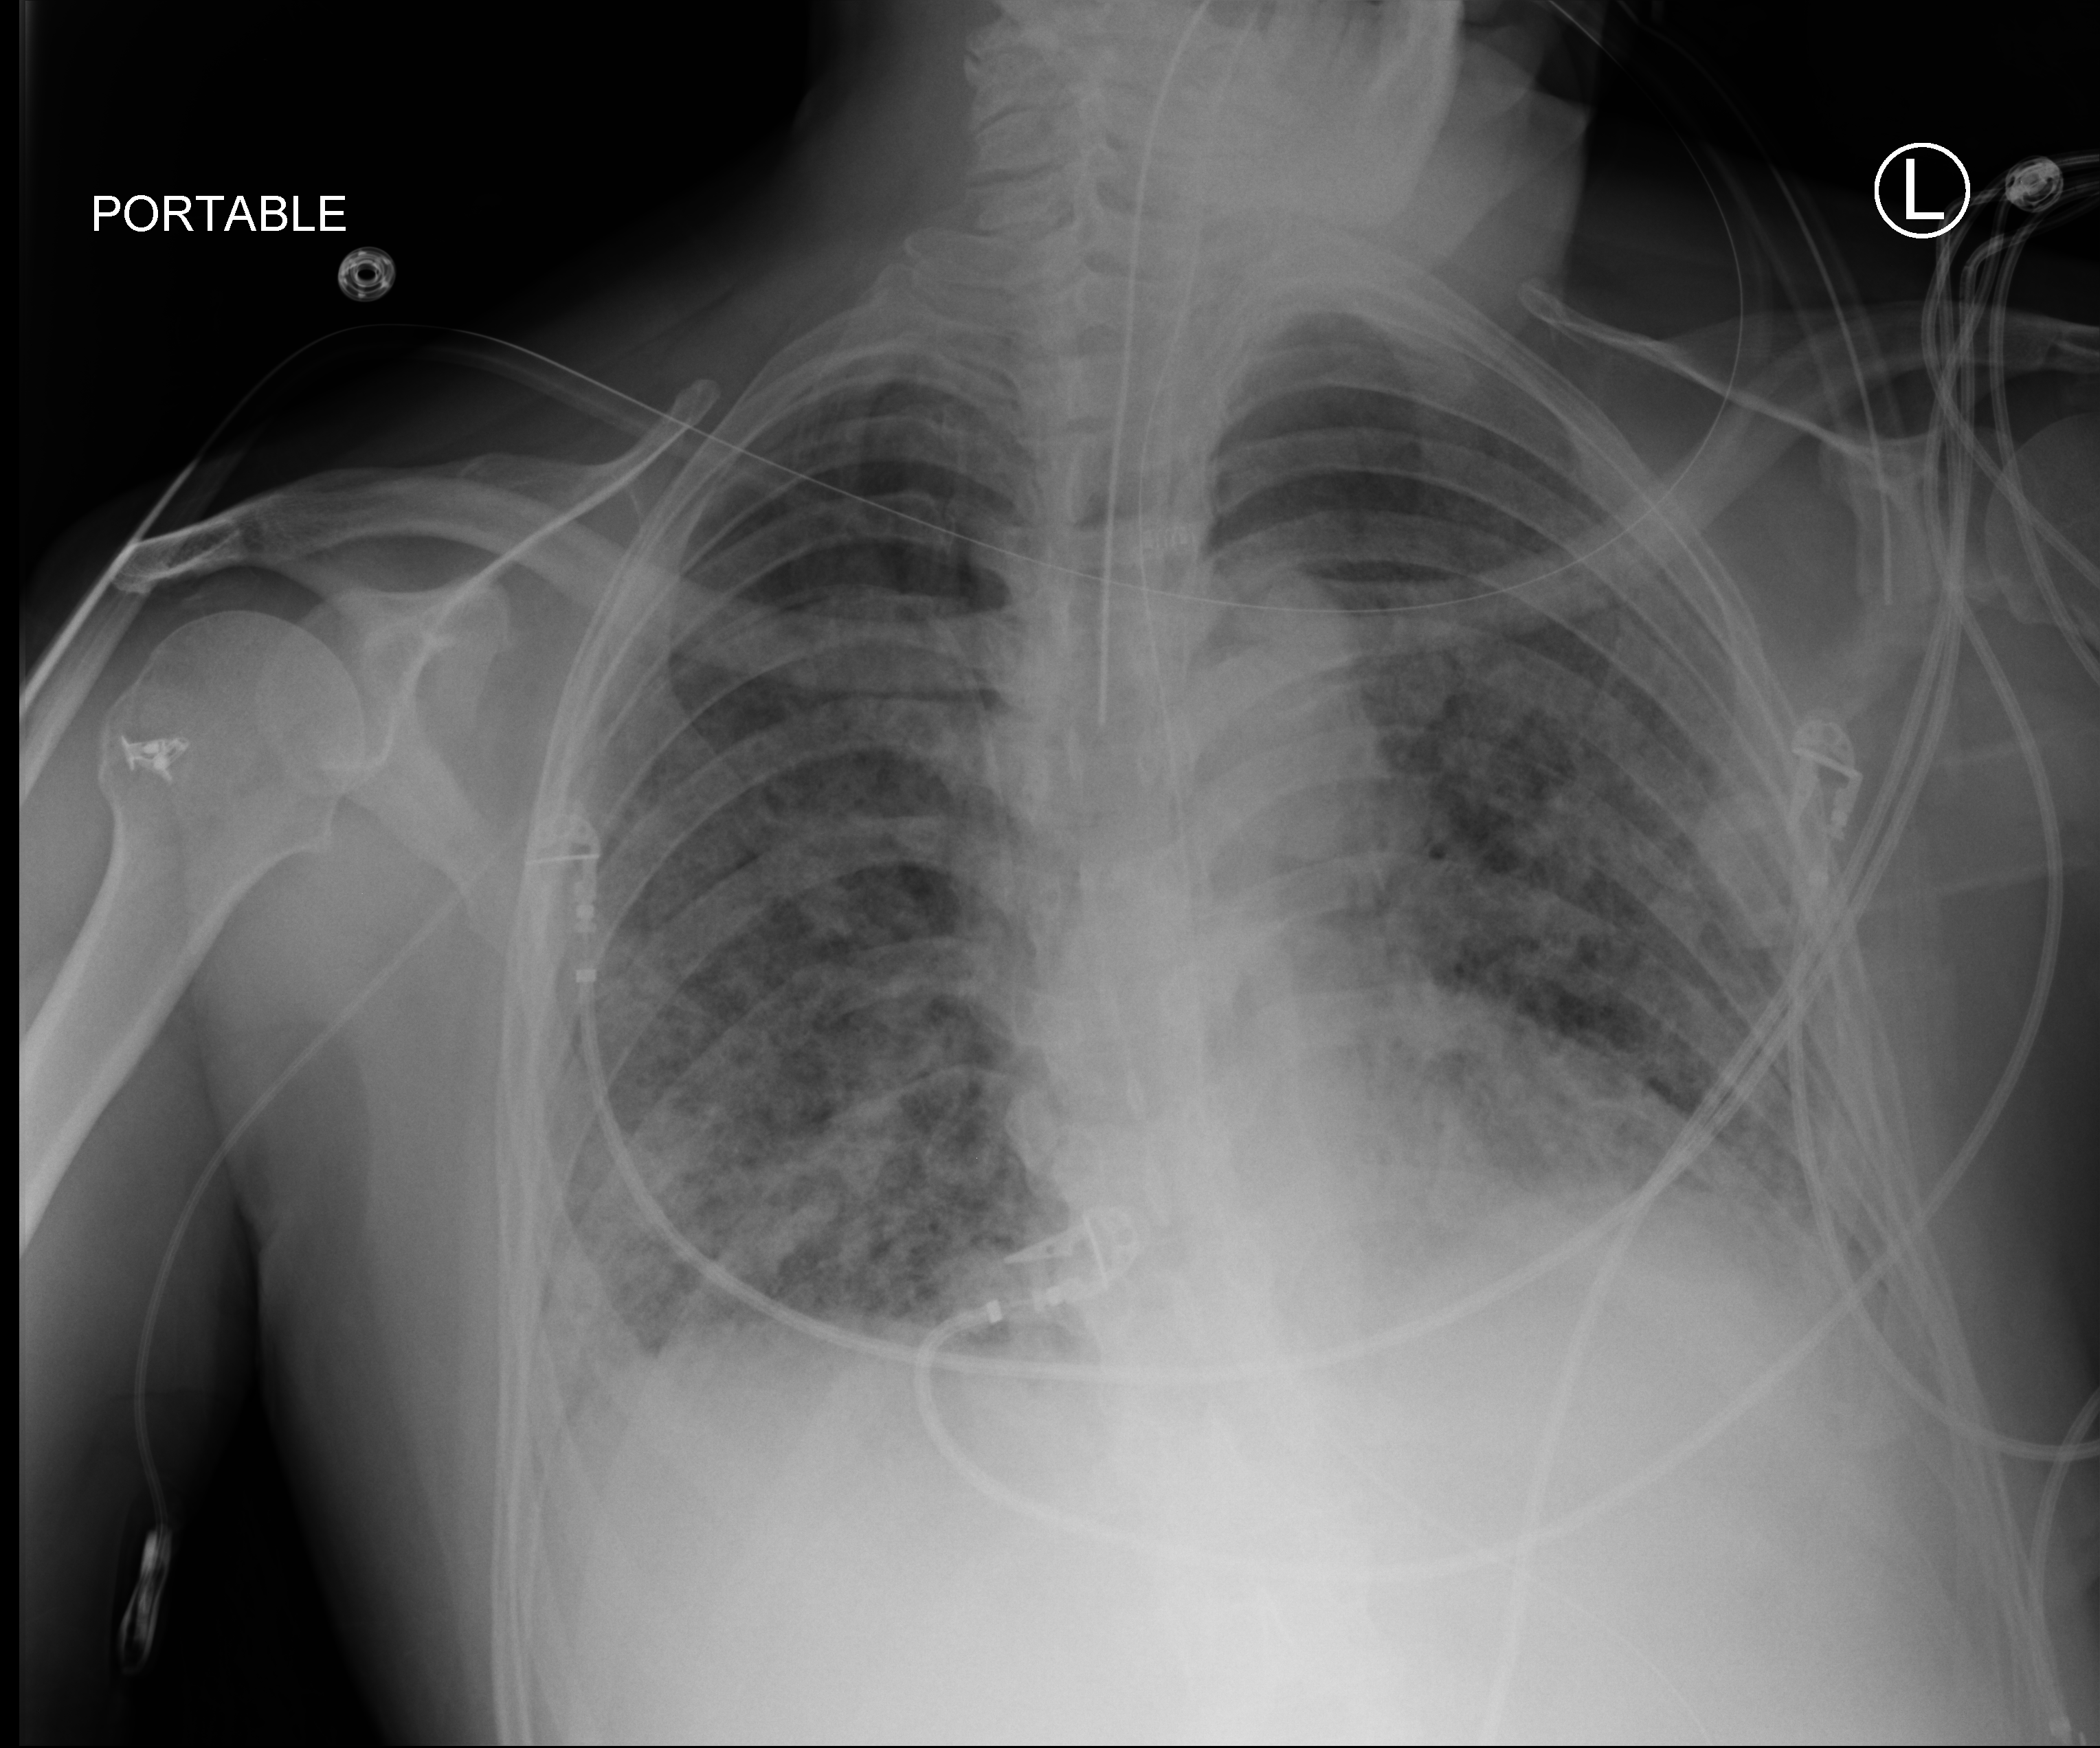
Bedside chest radiograph (computed radiography), anteroposterior (AP) projection. Male patient hospitalised with COVID-19, age 60–74 years.
From the hospital-stay record, not from the radiograph (when in the stay this image was taken is not recorded):
- chronic kidney disease (admission record): no
- admitted to intensive care during this hospital stay: yes
- mechanically ventilated during this hospital stay: yes